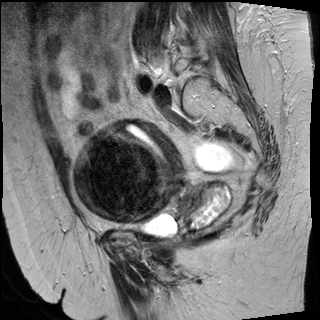
Pelvic MRI for cervical cancer, one sagittal slice; position 20 of 50 along the scan axis; T2-weighted; 1.5 T; TE 89 ms, TR 4880 ms; 320 × 320 image matrix, field of view 260 × 260 mm. Patient: female, 50 years.
Structures marked on this image (expert manual segmentation):
- uterus and cervix: bounding box <71,119,229,230> (left, top, right, bottom; pixels)